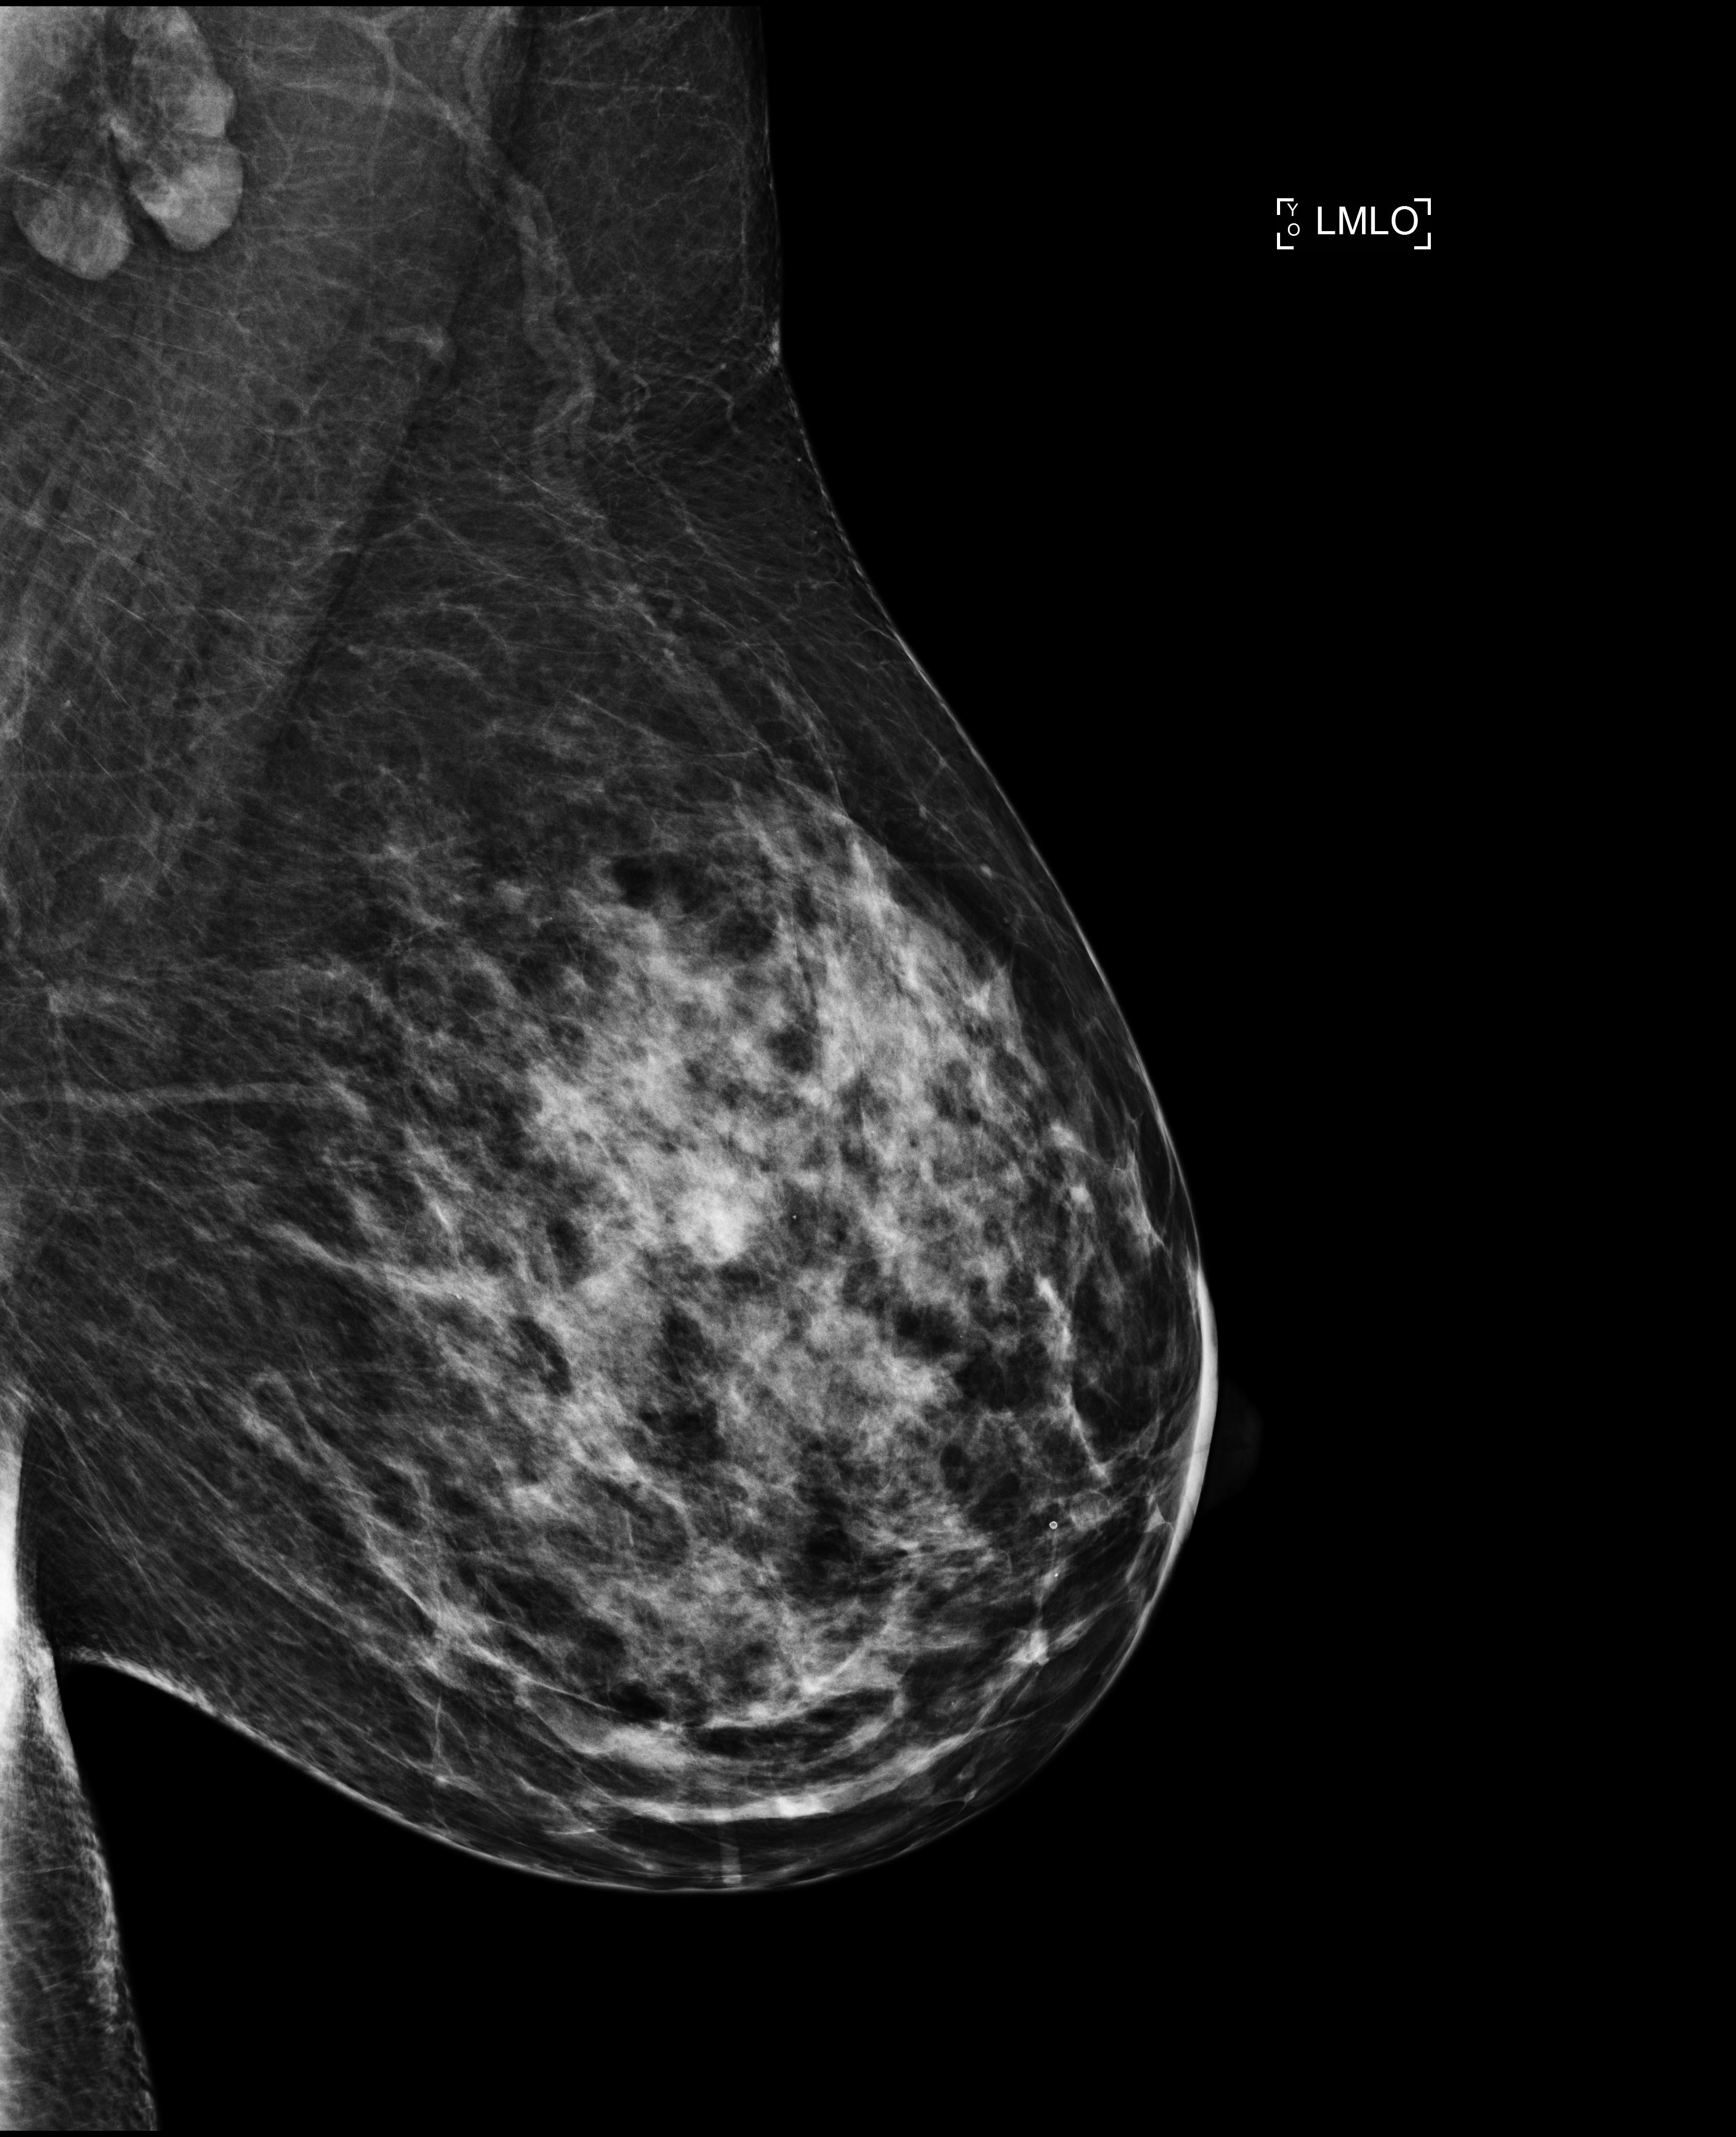
Digital mammogram (FFDM); left breast; mediolateral oblique (MLO) view; screening examination; compressed breast thickness 75 mm; system: Selenia Dimensions. Patient aged 45 years (female).
- BI-RADS breast density category at the screening exam (both breasts, scale 1–4): 3
- final BI-RADS assessment for this screening round (tomosynthesis exam, both breasts): category 2
- recall: no recall after this screen